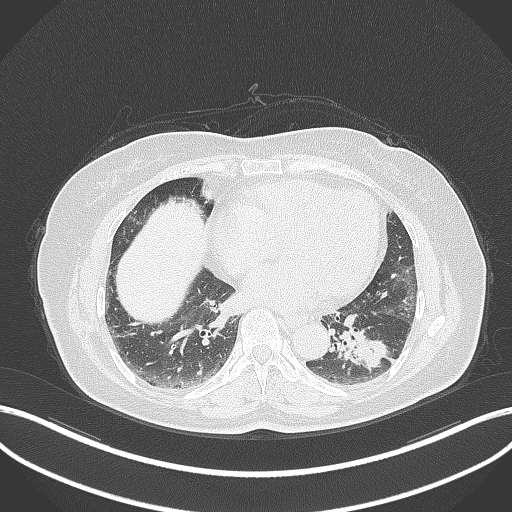
Chest CT, one axial slice. Position 145 of 311 along the scan axis. 120 kVp. Lung window (W 1500 / L -600 HU). 1 mm slice thickness. 512 × 512 image matrix. Patient: female, 59 years. Case-level facts recorded for this patient, not image findings: clinical TNM (as recorded): T2a N0 M0.
Structures marked on this image (rectangle marked by the reading radiologist):
- lung tumour (recorded histology: adenocarcinoma): bounding box <334,325,389,367> (left, top, right, bottom; pixels)